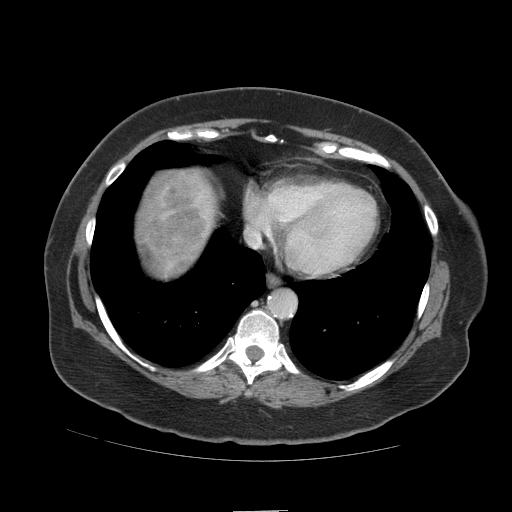
Contrast-enhanced abdominal CT (liver protocol), one axial slice. Position 100 of 109 along the scan axis. Soft-tissue window (W 400 / L 40 HU). 2.5 mm slice thickness. 512 × 512 image matrix, field of view 420 × 420 mm. Case-level facts recorded for this patient, not image findings: diagnosis: hepatocellular carcinoma (patient treated with transarterial chemoembolisation; whether this scan precedes or follows treatment is not stated here); TNM stage (as recorded): Stage-IVB.
Annotated regions visible in this slice (semi-automatic segmentation, software-assisted and operator-edited):
- liver parenchyma outside the tumour (the mass and vessels are separate outlines, so this box may not span the whole liver): bounding box (x1, y1, x2, y2) in pixels: (142, 168, 216, 252)
- mass: (134, 169, 216, 277)